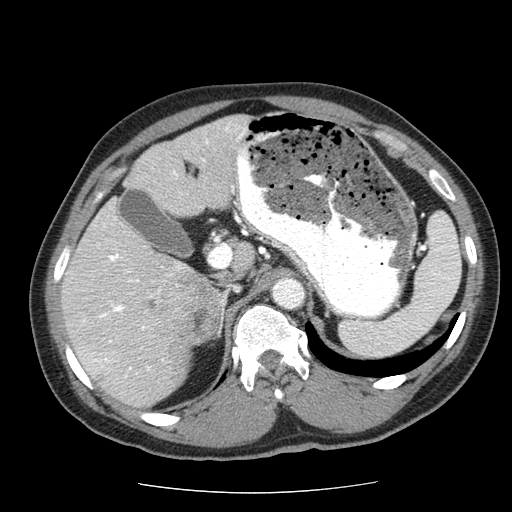
Contrast-enhanced abdominal CT (liver protocol), one axial slice; reconstruction kernel STANDARD; soft-tissue window (W 400 / L 40 HU); 512 × 512 image matrix, field of view 360 × 360 mm. From the clinical record (not read from this slice): diagnosis: hepatocellular carcinoma (patient treated with transarterial chemoembolisation; whether this scan precedes or follows treatment is not stated here); TNM stage (as recorded): Stage-IIIA; Child-Pugh class: A; tumour differentiation: well differentiated; tumour nodularity: multinodular.
Outlined on this slice (semi-automatically segmented with operator editing):
- abdominal aorta: box from (x=274, y=278) to (x=303, y=306) px
- liver parenchyma outside the tumour (the mass and vessels are separate outlines, so this box may not span the whole liver): (x=60, y=114)–(x=249, y=407)
- mass: (x=144, y=271)–(x=223, y=343)
- liver vessels: (x=84, y=127)–(x=246, y=377)